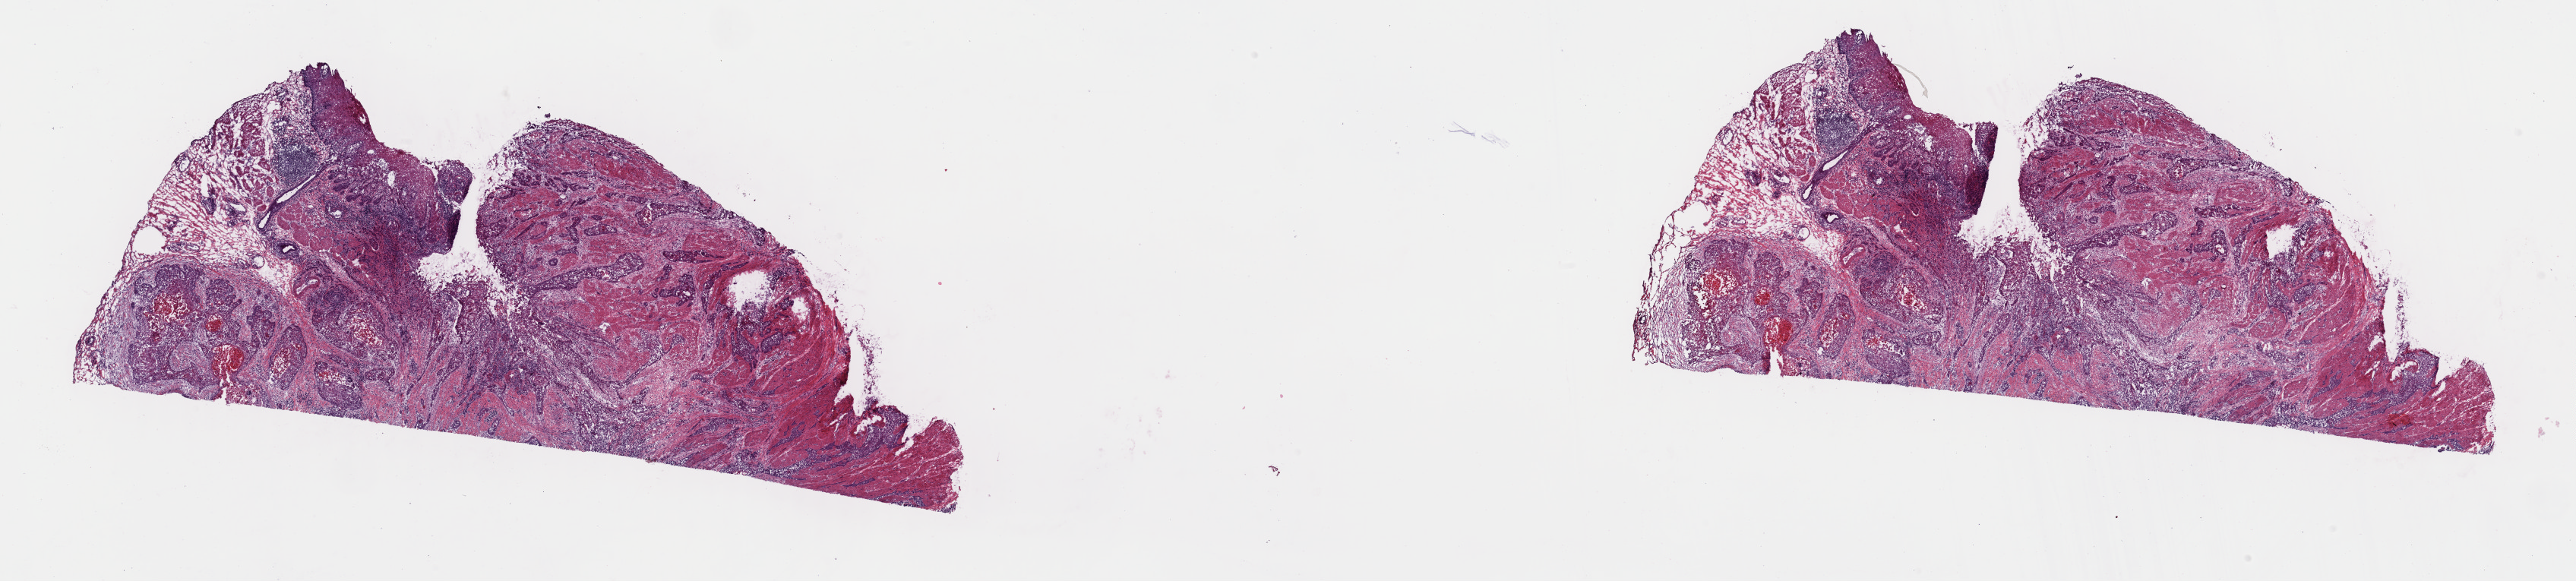
Digitized H&E tissue section (whole slide) — shown as a low-resolution overview of the whole scanned area (about 26.8 x 6.0 mm, from a 40x scan), frozen section from the top of the tissue portion, sample: primary tumour, esophagus. Male patient; age at initial diagnosis 50 years. Histologic grade: G2 (moderately differentiated). Slide review estimates, as recorded: tumour cells 30%, tumour nuclei 60%, normal cells 12%, stromal cells 40%, necrosis 18%. Inflammatory infiltration, as recorded: lymphocyte infiltration 5%, monocyte infiltration 1%, neutrophil infiltration 1%.
Diagnosis: Squamous cell carcinoma, NOS (middle third of esophagus). AJCC pathologic stage: IIB.